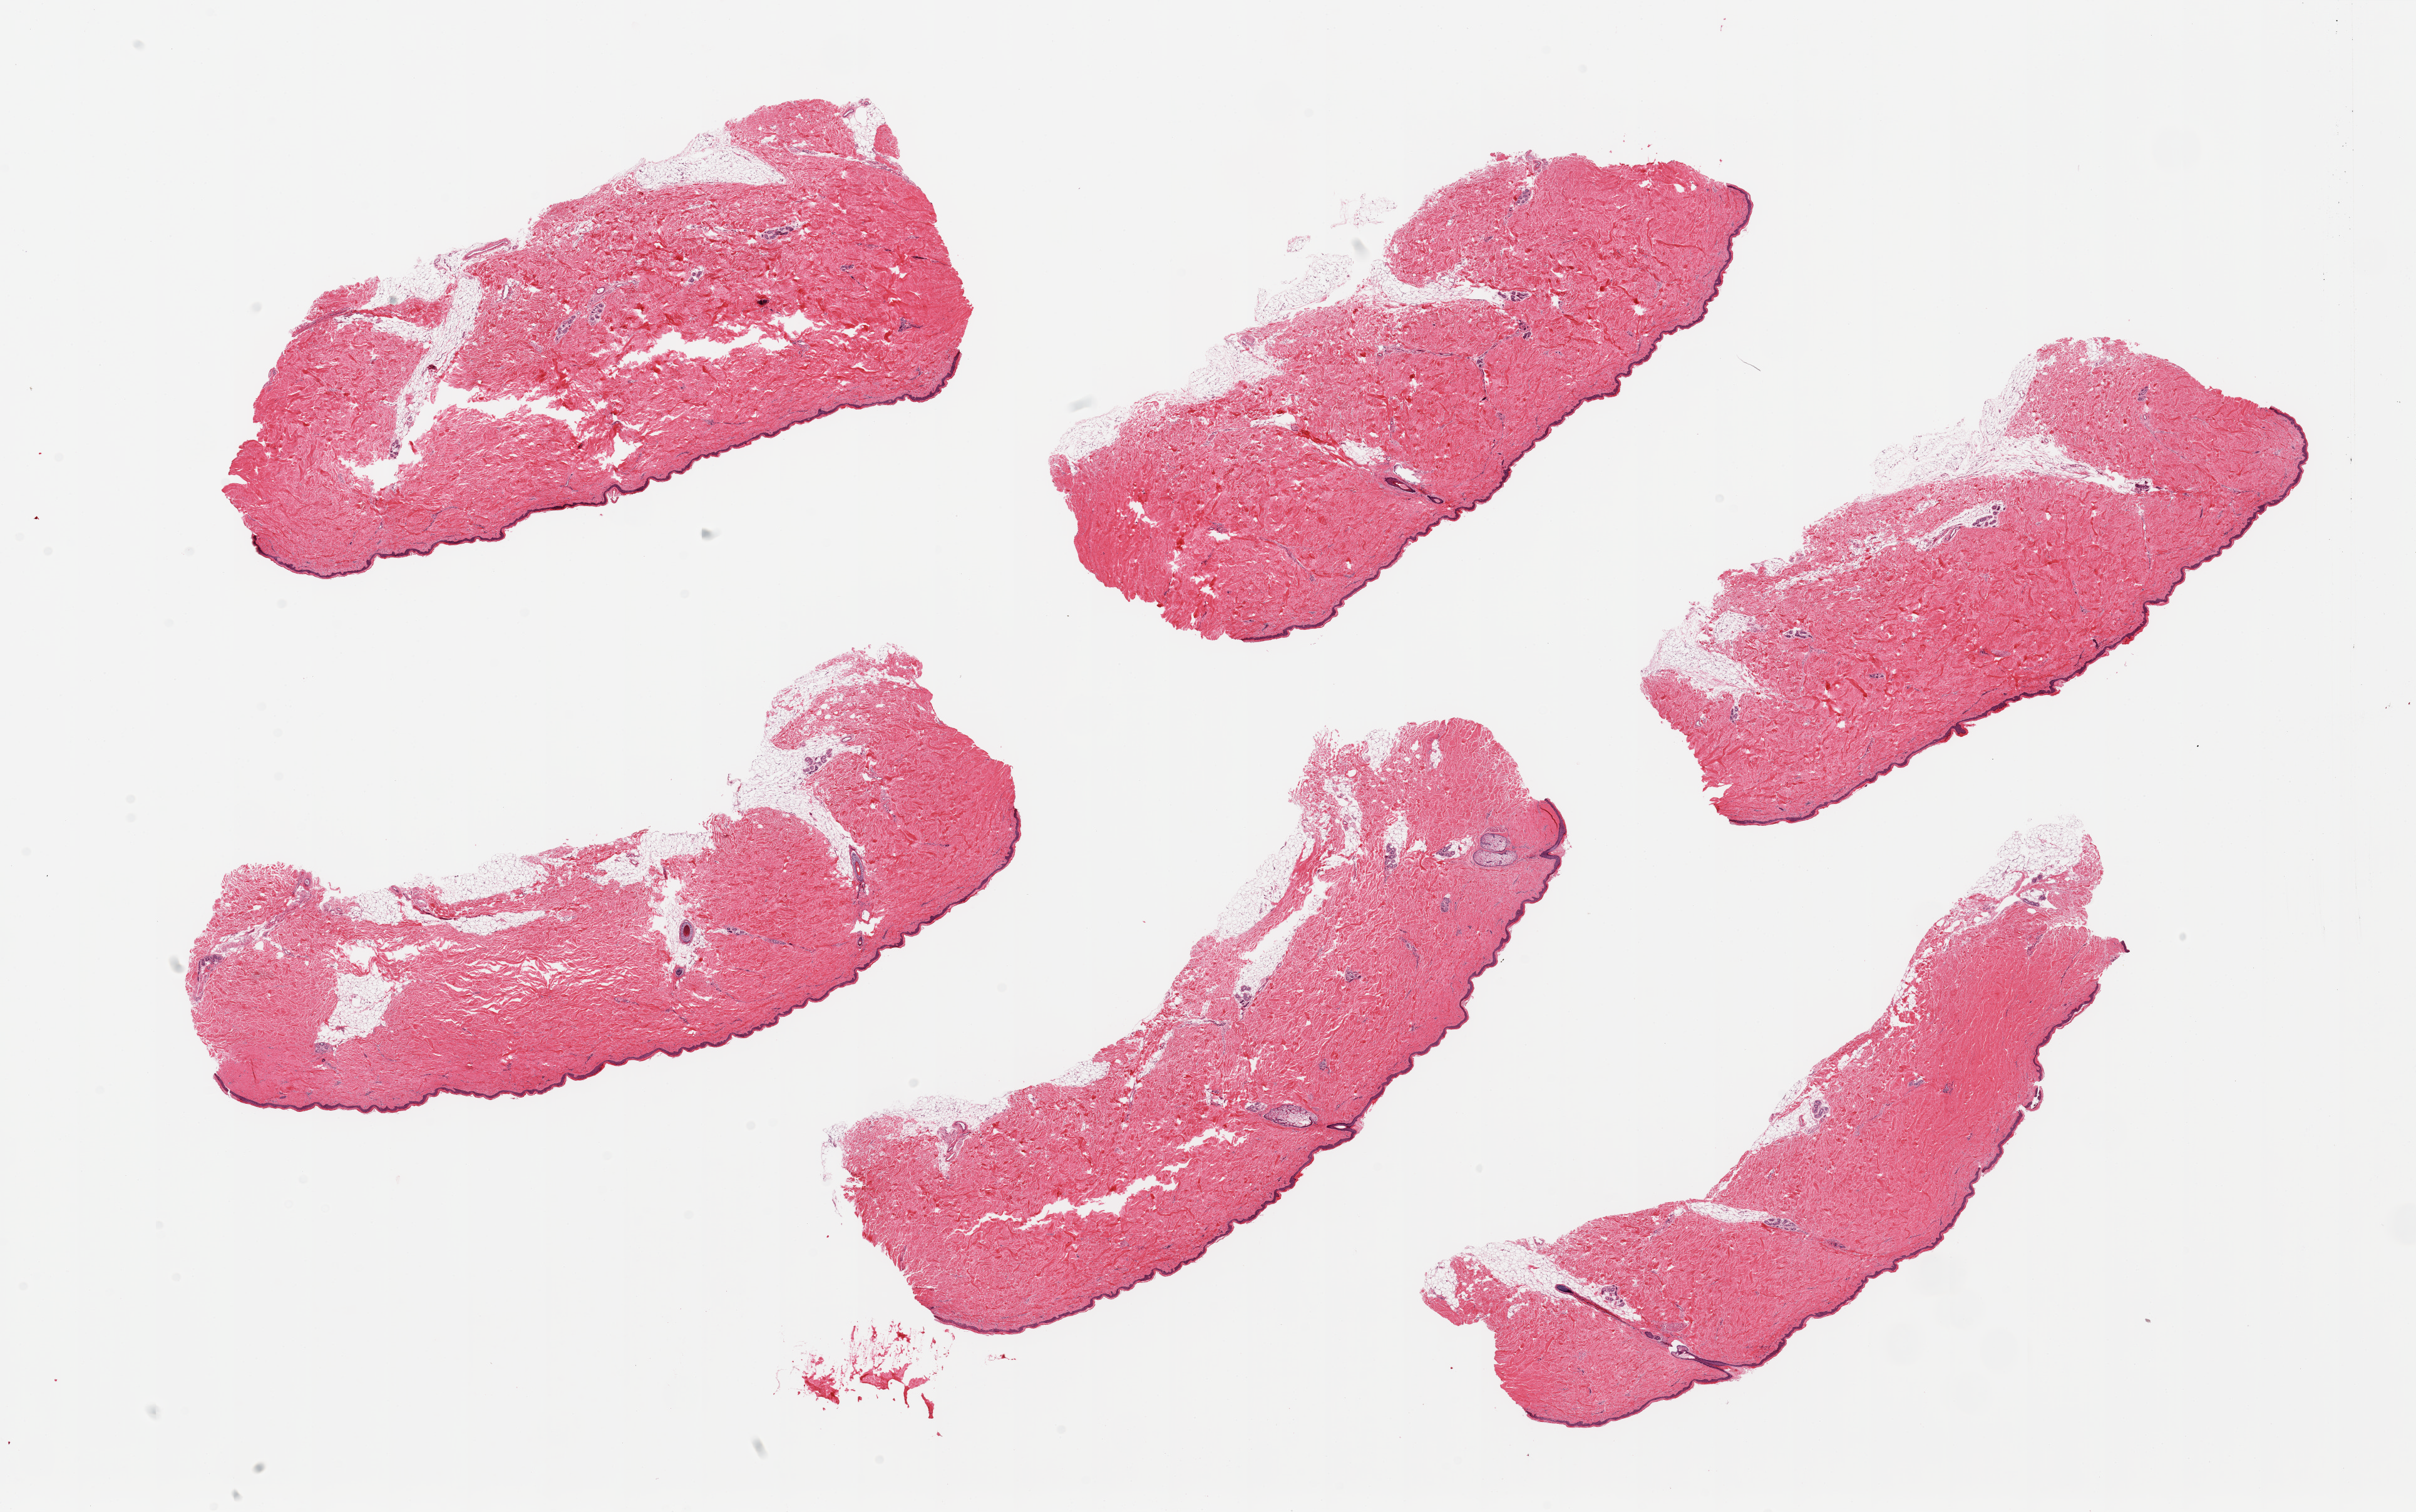
Whole-slide image, haematoxylin and eosin stain — low-resolution overview of the scanned area, about 30.5 x 19.1 mm. PAXgene-fixed paraffin-embedded (PFPE) section. Target tissue: skin of suprapubic region. Tissue donor sample. Donor sex: female.
Review note (as recorded): 6 pieces, trace adherent dermal fat; squamous epithelium is ~40-50 microns.